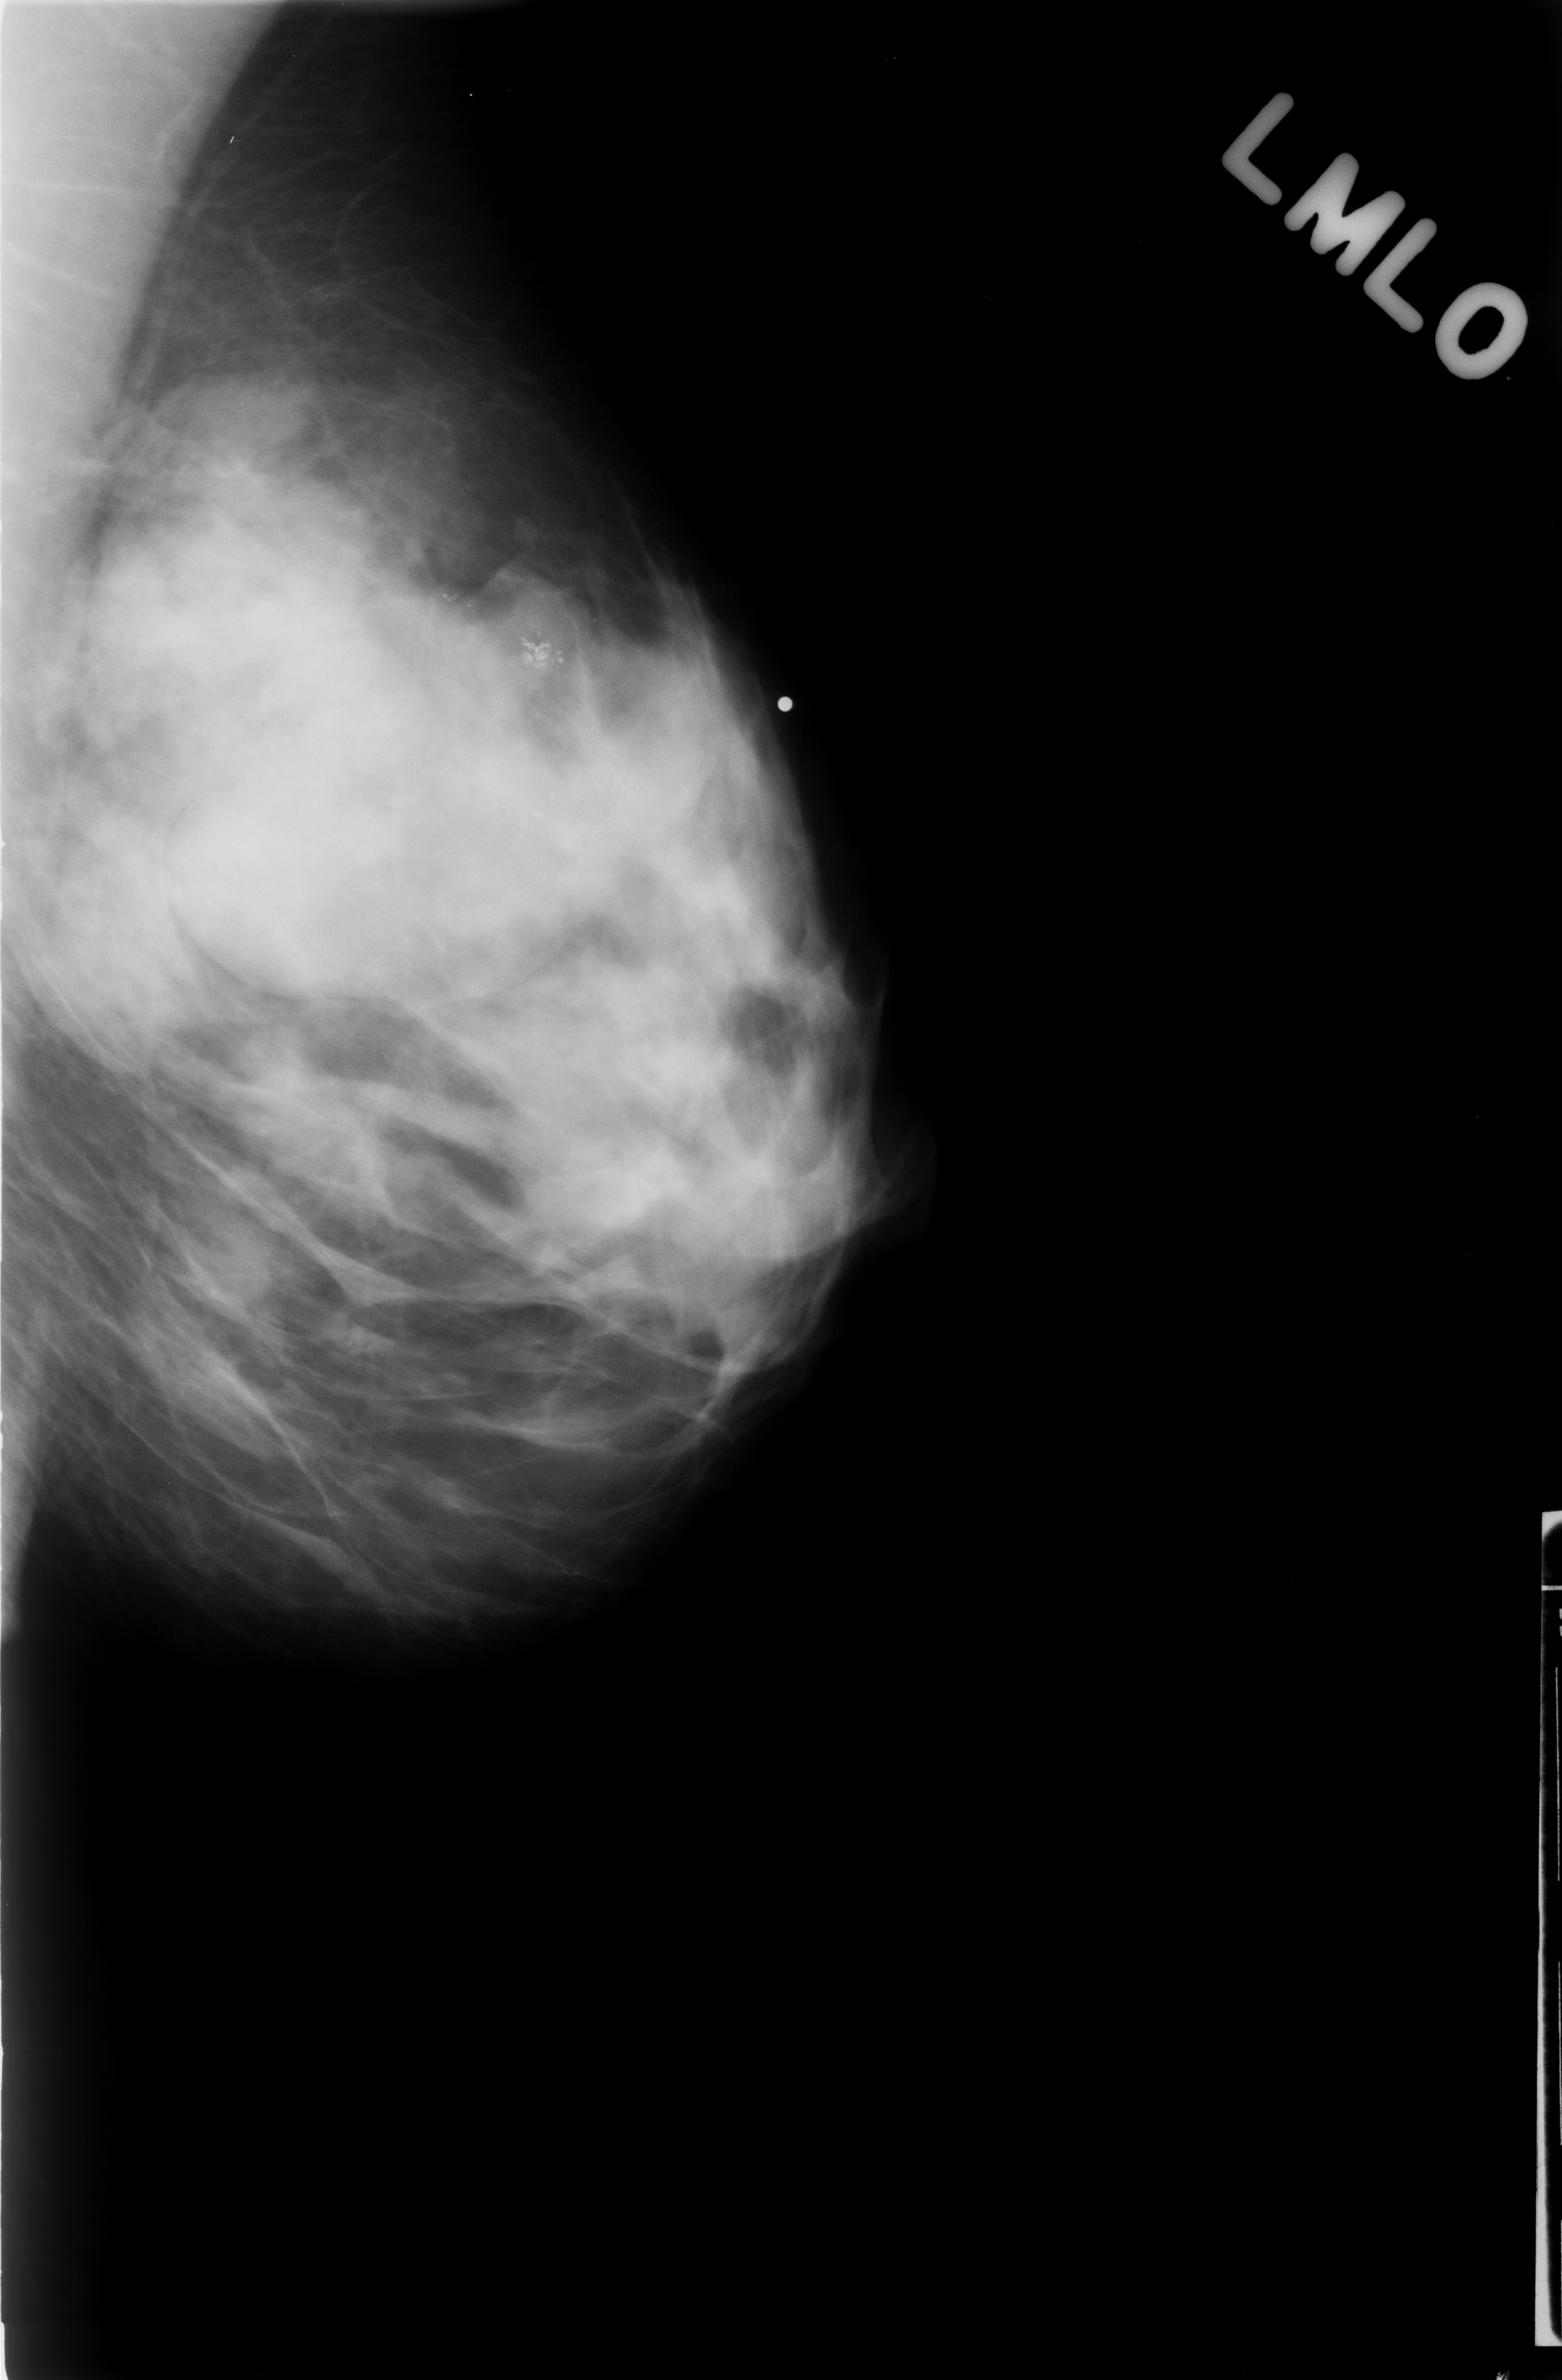
Digitized screen-film mammogram; left breast; MLO view; breast composition: heterogeneously dense (BI-RADS density category 3 of 4); 1562 × 2380 image matrix.
Expert-marked regions of interest on this image (one box per marked abnormality):
- mass, shape oval, margins obscured; BI-RADS assessment category 3; subtlety rating 4 on a 1 (subtle) to 5 (obvious) scale; pathology (as recorded): benign: bounding box (x1, y1, x2, y2) in pixels: (193, 719, 571, 1006)